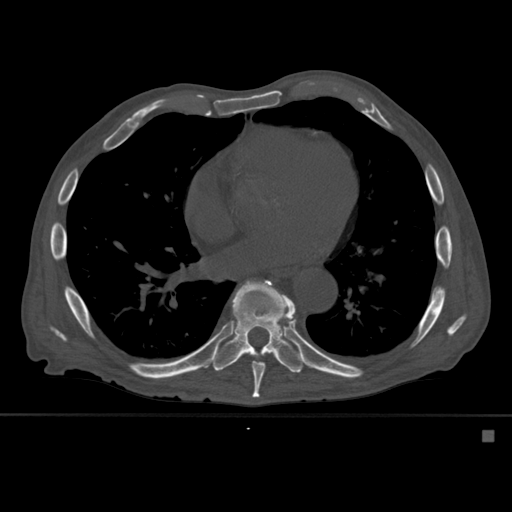
CT including the spine, one axial slice. Position 340 of 527 along the scan axis. Bone window (W 1800 / L 400 HU). 1.5 mm slice thickness. 512 × 512 image matrix. Patient: male, 78 years. Case-level facts recorded for this patient, not image findings: primary cancer: prostate.
Annotated regions visible in this slice (semi-automatically segmented with operator editing):
- T8 vertebra: bounding box [x1, y1, x2, y2] px = [250, 280, 265, 398]
- T9 vertebra: [213, 280, 306, 373]